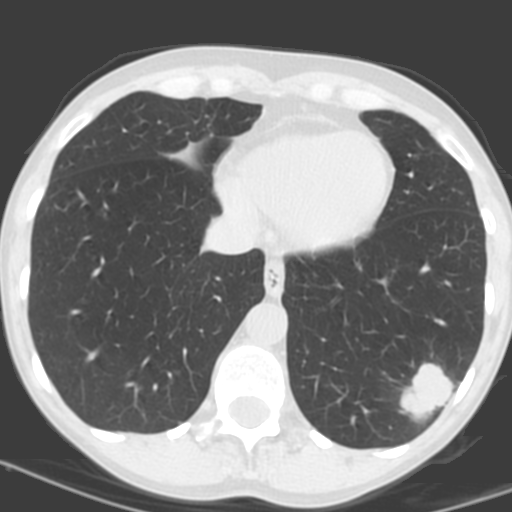
Low-dose screening chest CT, one axial slice. Position 46 of 156 along the scan axis. 120 kVp. Lung window (W 1500 / L -600 HU). 3.2 mm slice thickness. 512 × 512 image matrix.
Annotated regions visible in this slice (outlined manually by an expert reader):
- lesion 1 (tumor, lower lobe of left lung): bounding box [x1, y1, x2, y2] px = [401, 363, 455, 416]